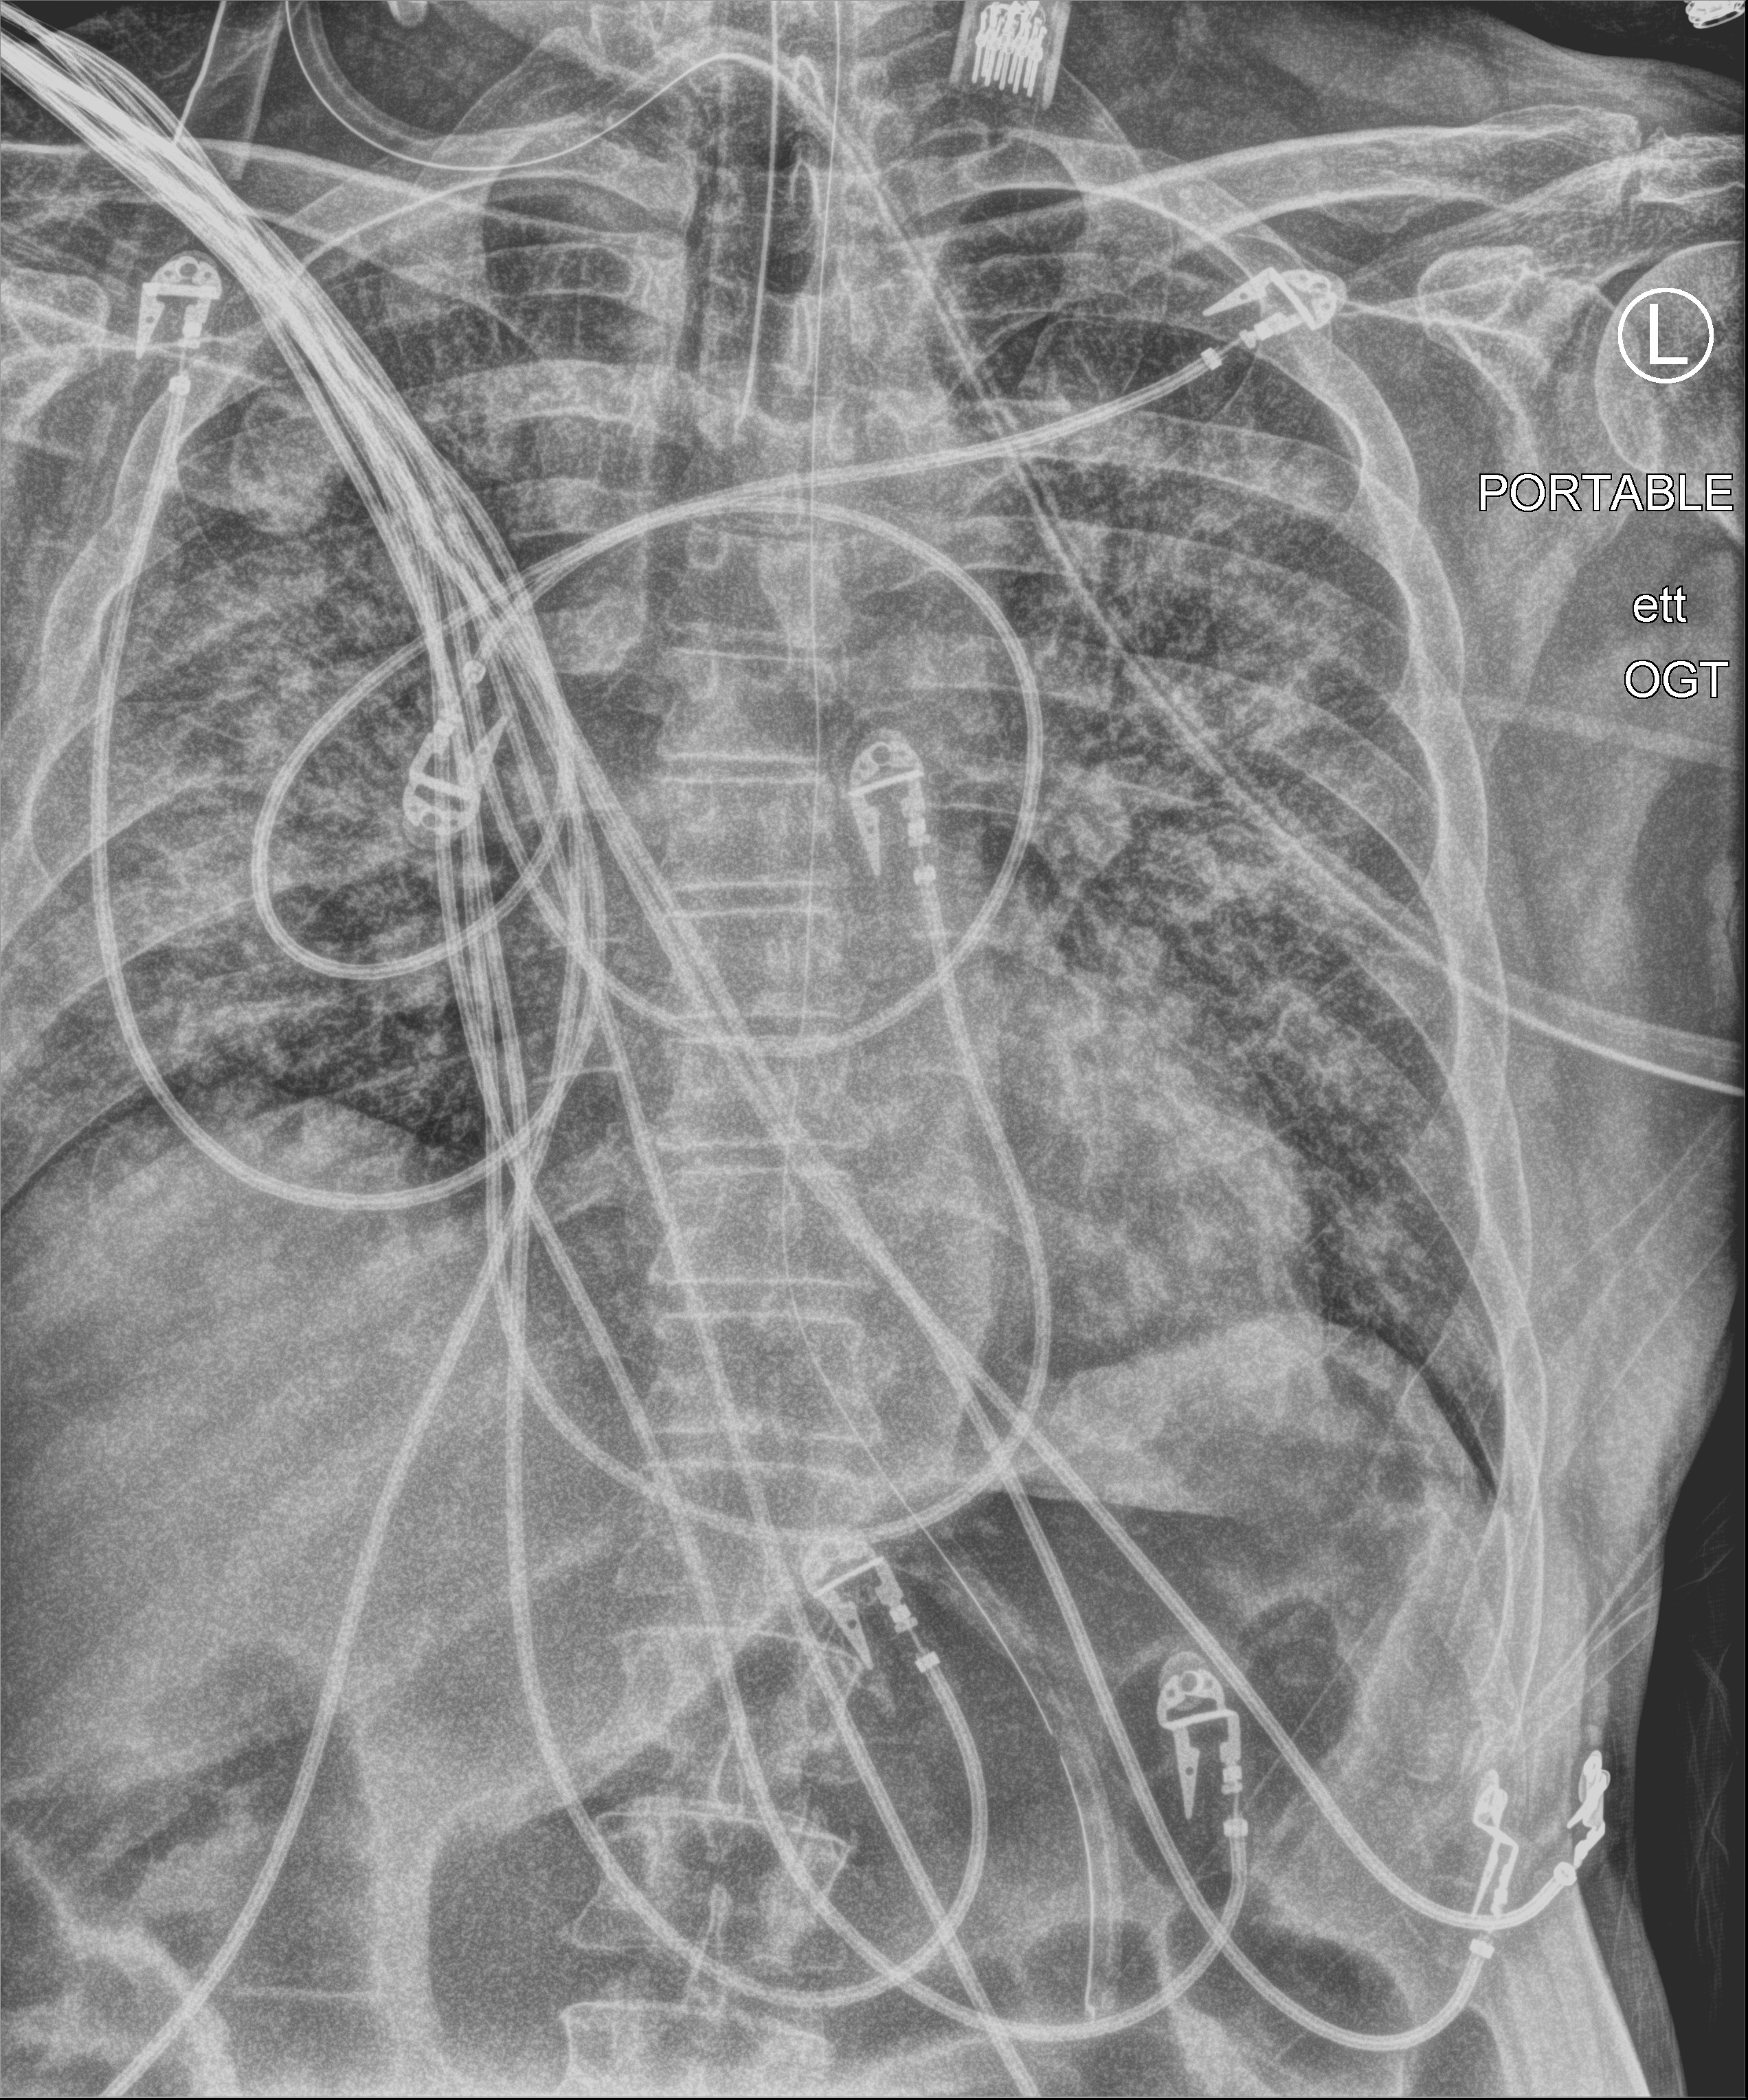
Bedside chest radiograph (computed radiography), anteroposterior (AP) projection. Patient hospitalised with COVID-19; male, aged 60–74 years.
Admission-level facts for this patient (not findings on this image; timing relative to this image not recorded): admitted to intensive care during this hospital stay: yes; mechanically ventilated during this hospital stay: yes.